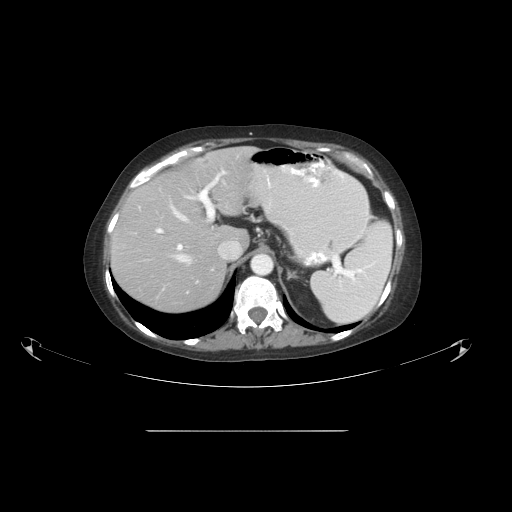
Contrast-enhanced abdominal CT, one axial slice; slice 37 of 51 in the series (ordered by position); reconstruction kernel STANDARD; 120 kVp; soft-tissue window (W 400 / L 40 HU); 5 mm slice thickness; 512 × 512 image matrix, field of view 475 × 475 mm. Female patient, age 48 years. Case-level facts recorded for this patient, not image findings: diagnosis: colorectal cancer liver metastases, imaged before liver resection; multiple liver metastases: yes; largest metastasis: 1 cm.
Outlined on this slice (expert manual segmentation):
- hepatic veins: bounding box <145,206,241,267> (left, top, right, bottom; pixels)
- liver: <112,148,256,314>
- planned liver remnant (the part of the liver to remain after resection): <112,168,232,314>
- portal vein (with intrahepatic branches): <156,170,226,283>
- liver metastasis: <203,160,209,167>